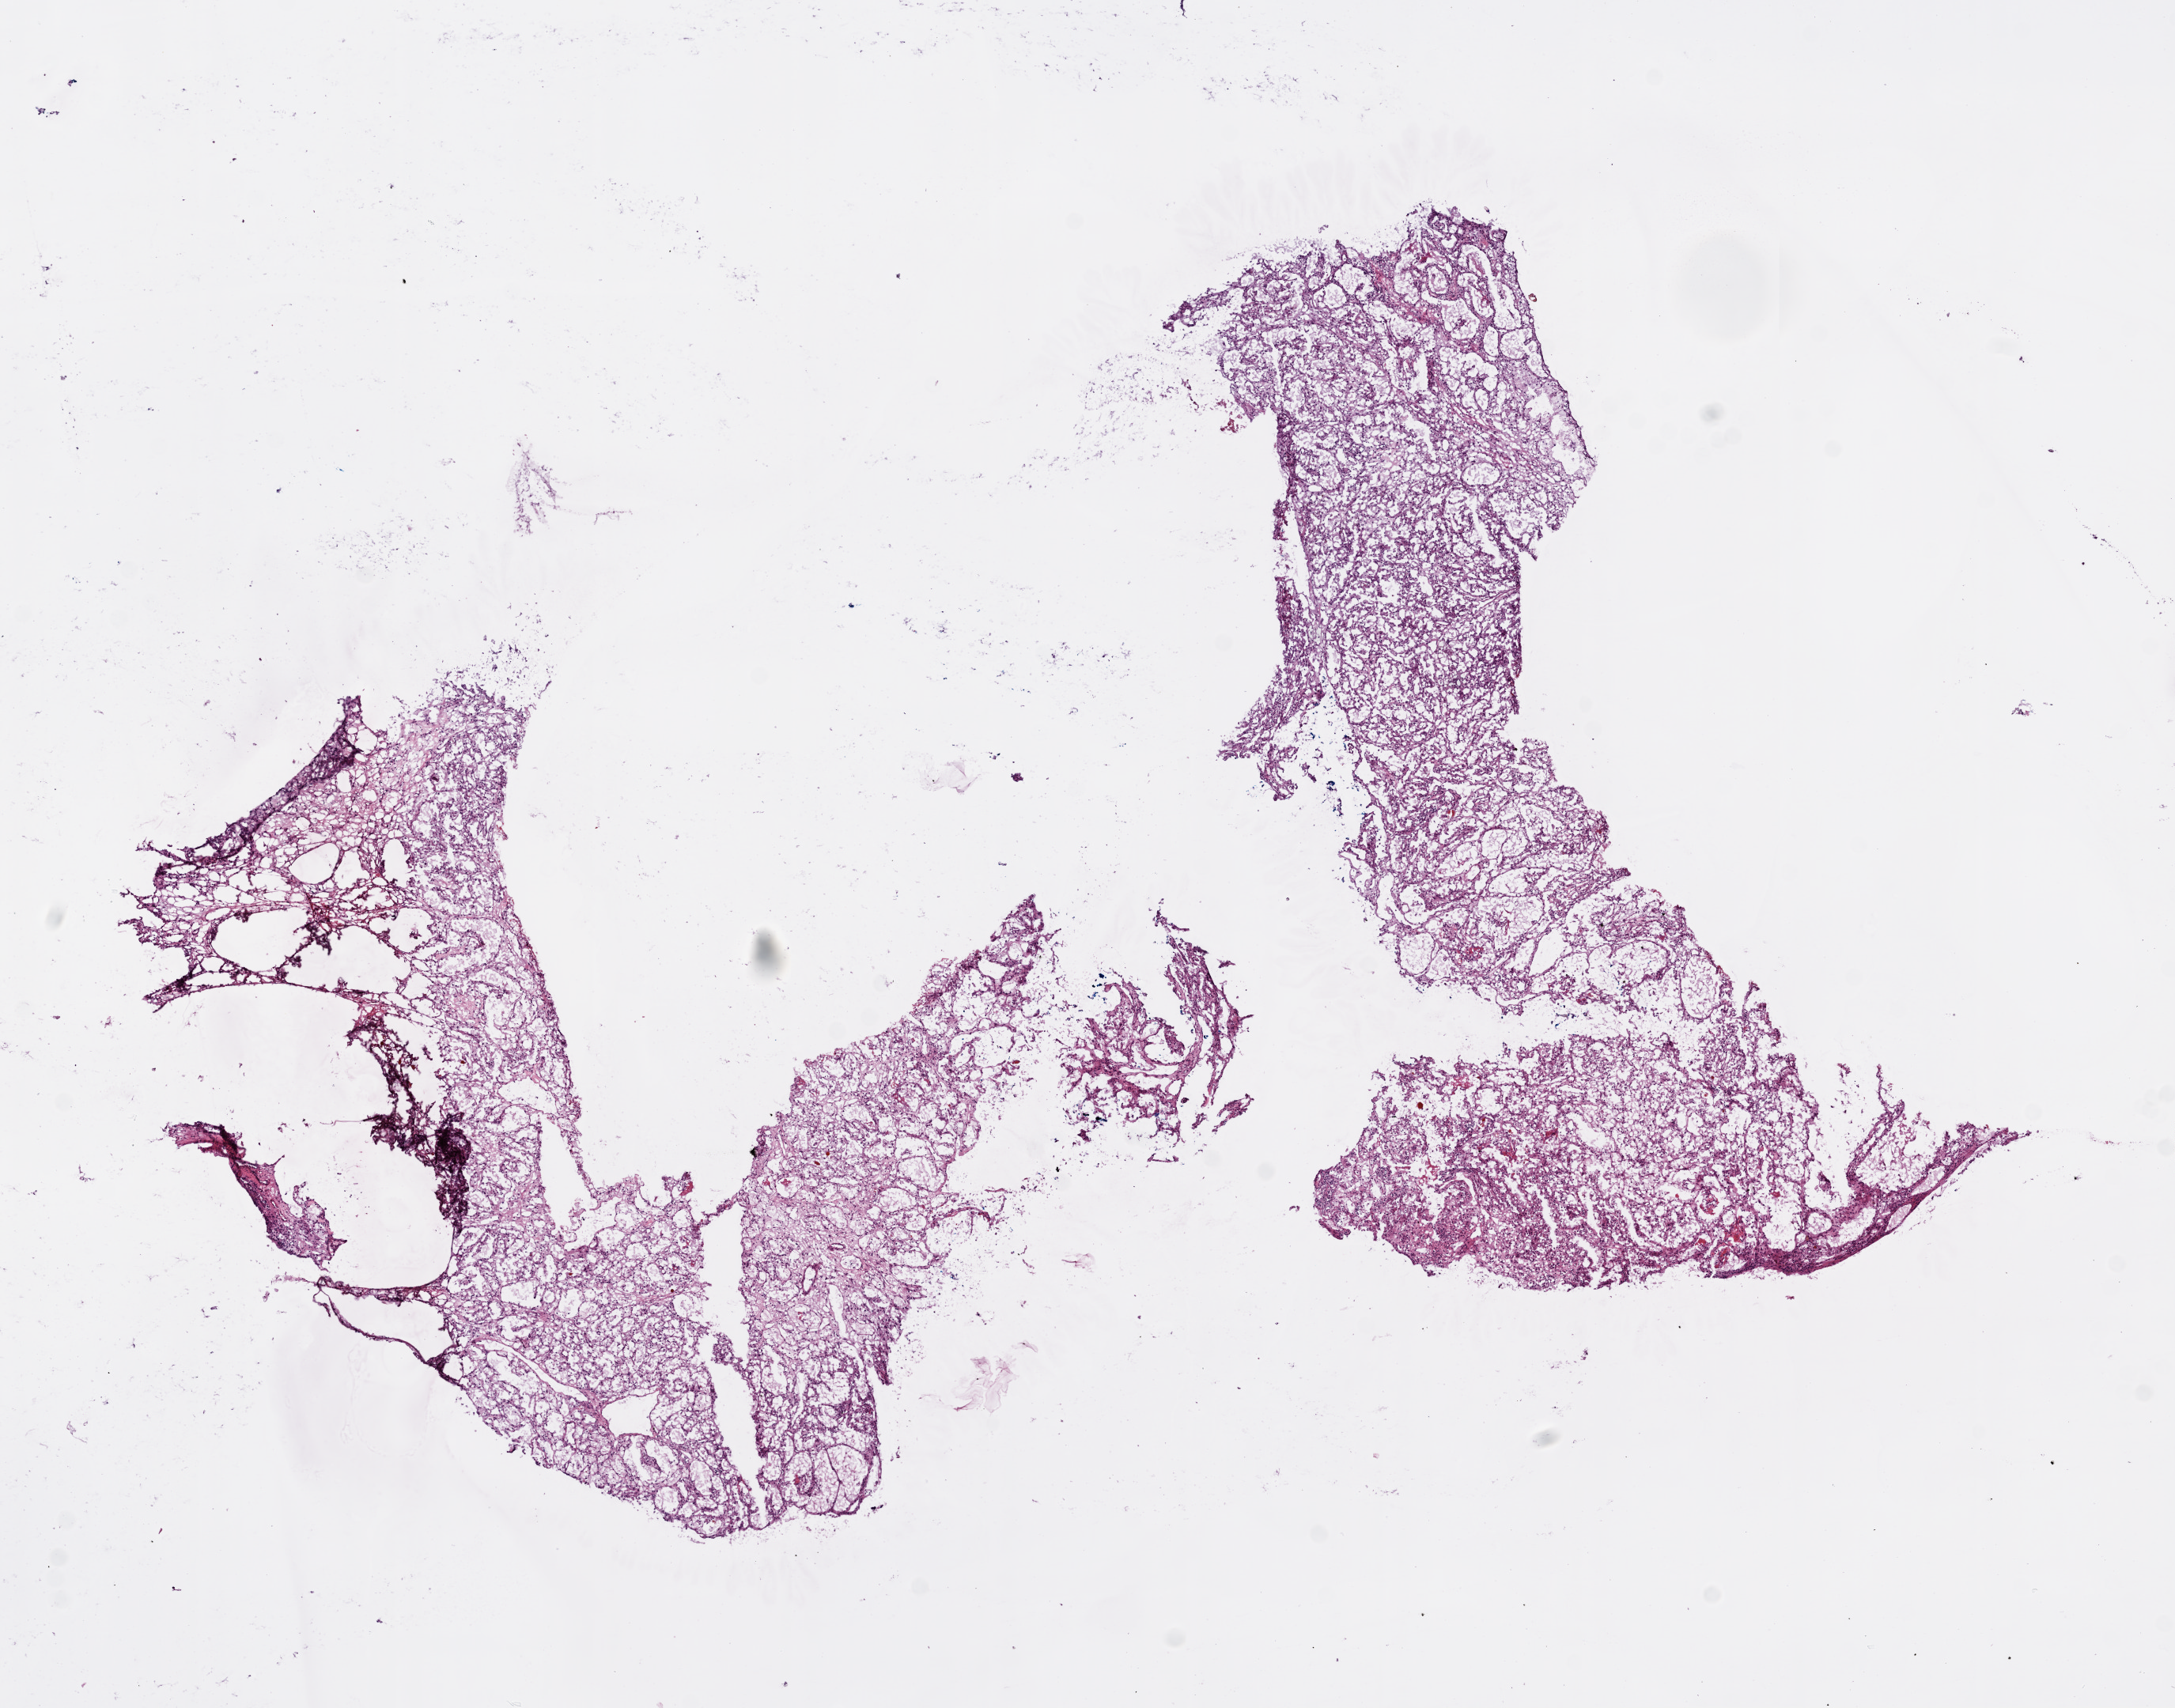
Whole-slide histology image, H&E — low-resolution overview of the scanned area, about 11.0 x 8.7 mm; frozen section; sample: primary tumour, kidney. Patient: female, age at initial diagnosis 55 years. Histologic grade: G2 (moderately differentiated). Composition of this section per pathologist review: tumour cells 92%, tumour nuclei 95%, normal cells 0%, stromal cells 5%, necrosis 3%.
Histologic diagnosis: Clear cell adenocarcinoma, NOS. Laterality: left. AJCC pathologic stage: I.